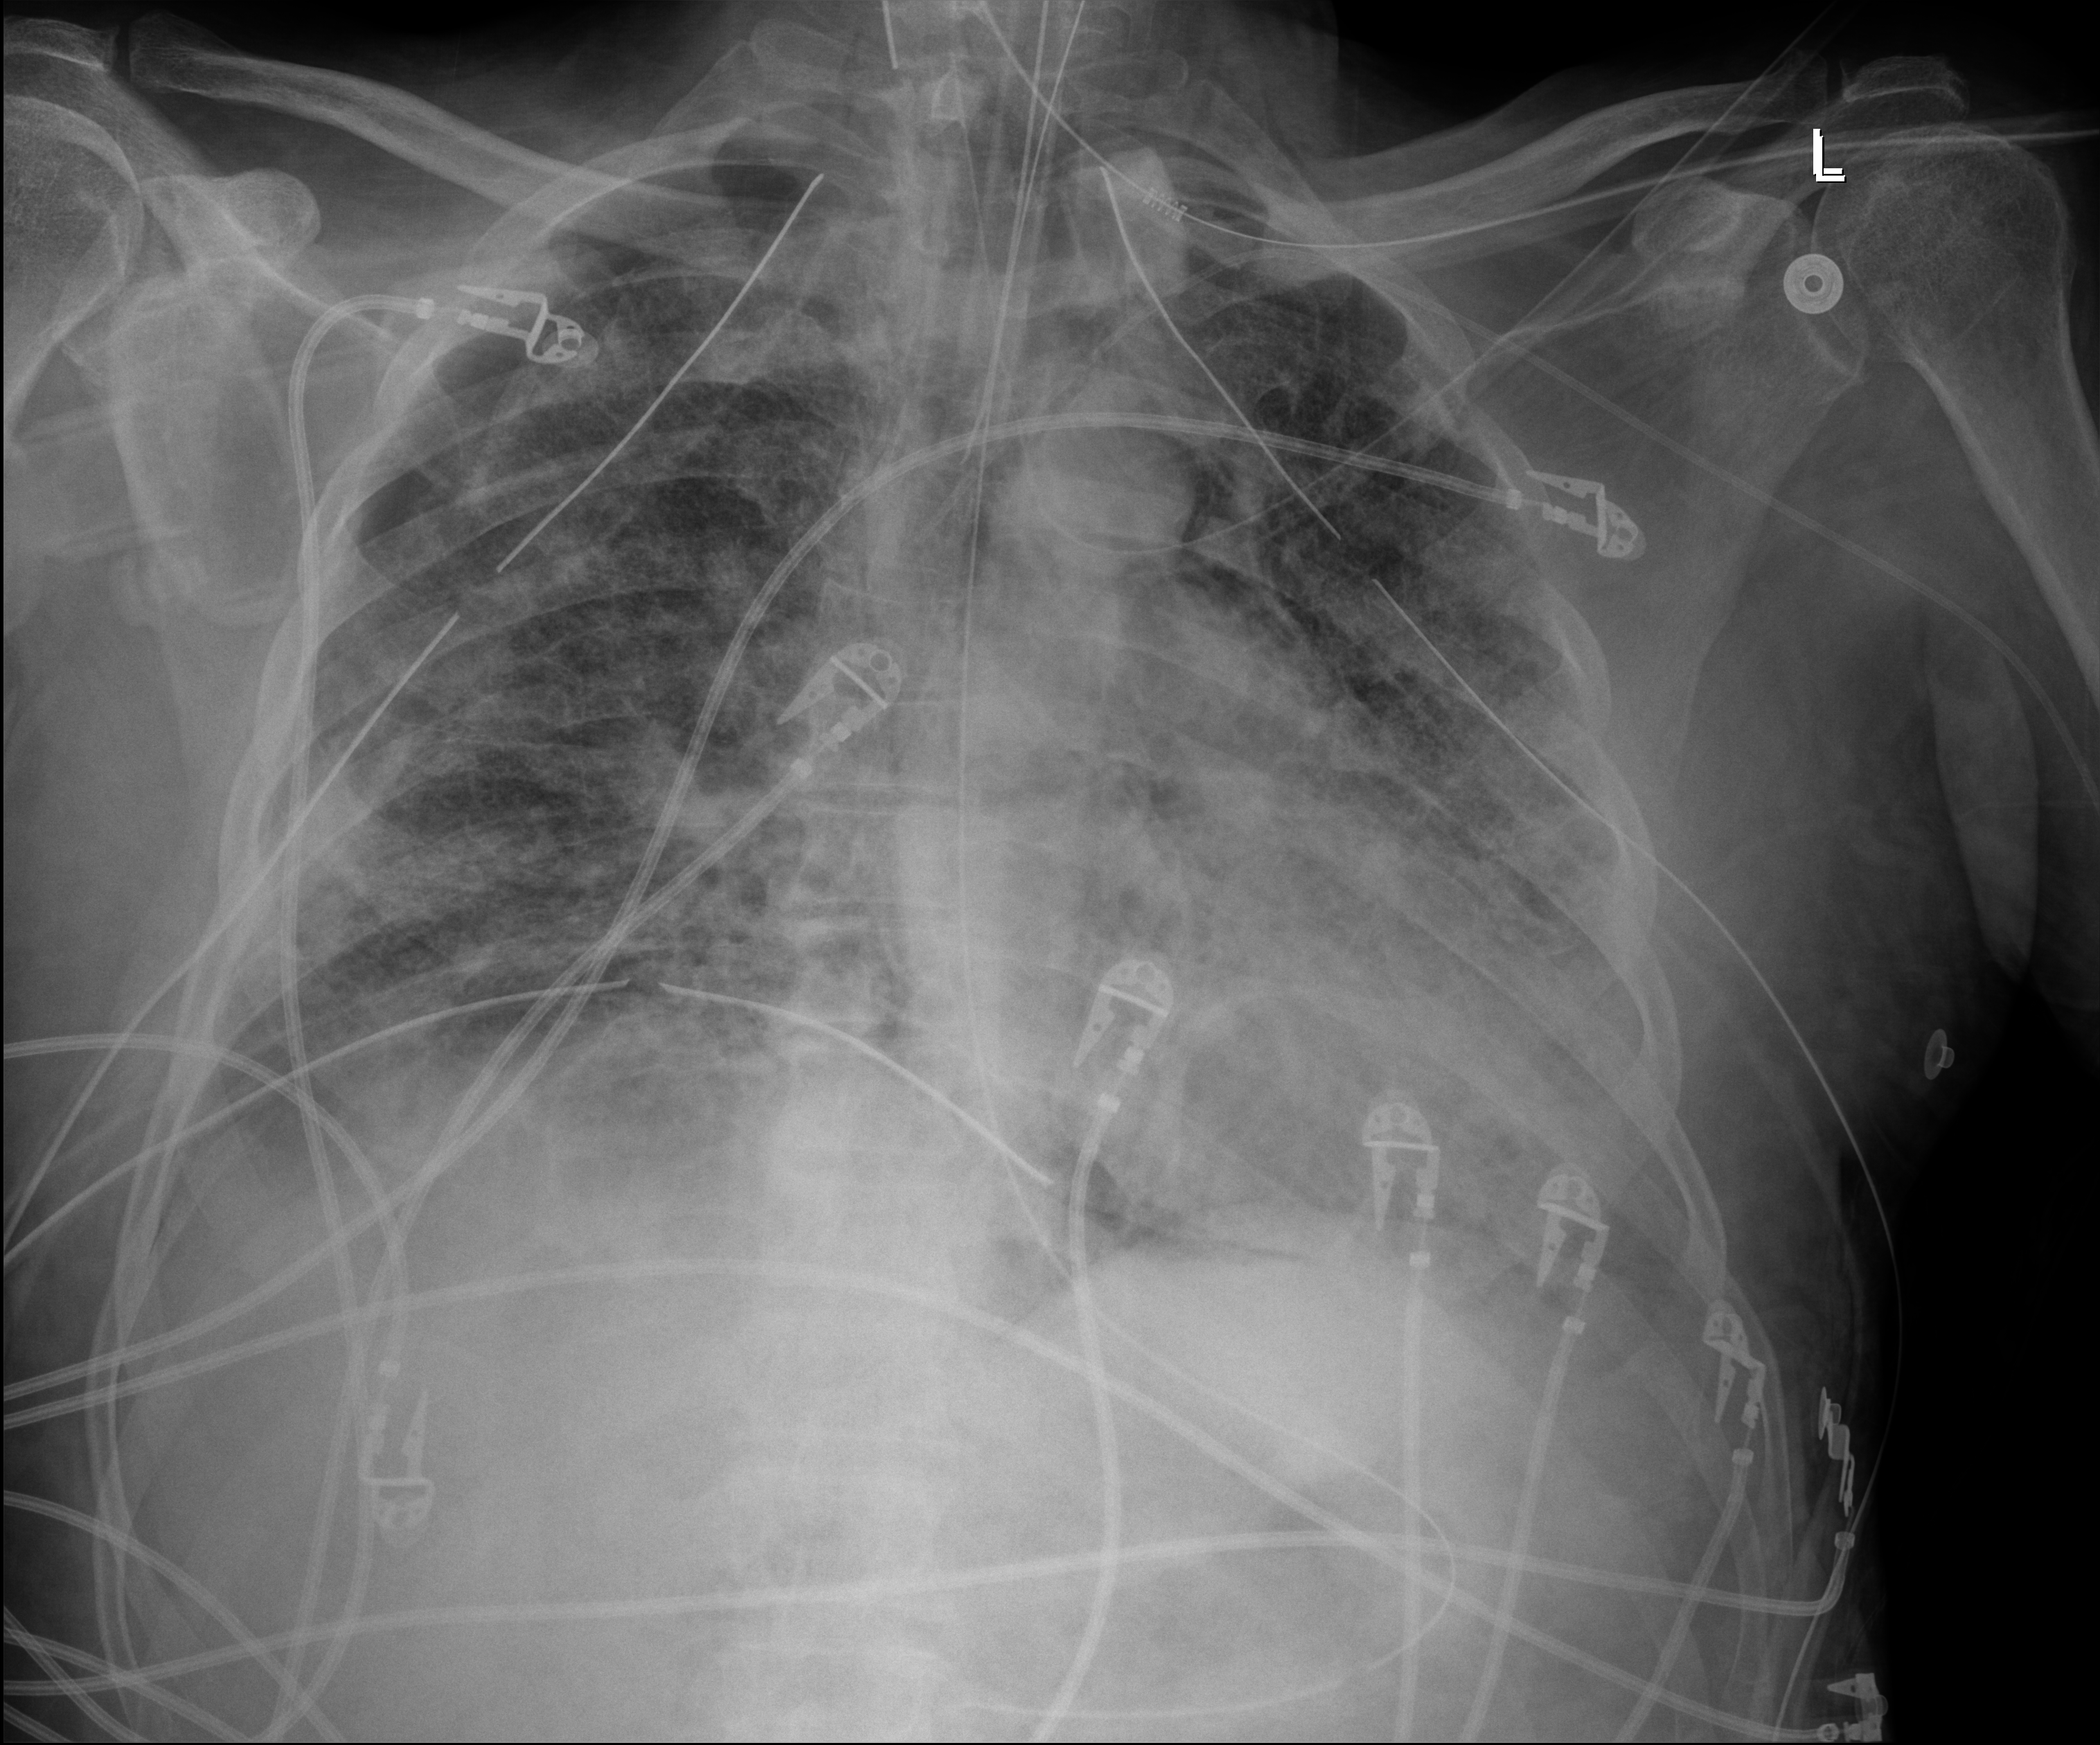
Portable chest radiograph; anteroposterior (AP) projection. Male patient hospitalised with COVID-19, age 18–59 years.
From the hospital-stay record, not from the radiograph (when in the stay this image was taken is not recorded): admitted to intensive care during this hospital stay: yes.